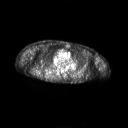
FDG PET of an extremity soft-tissue mass (from a PET/CT study), one axial slice; 3.27 mm slice thickness; 128 × 128 image matrix, field of view 700 × 700 mm. Patient: male, 61 years. From the clinical record (not read from this slice): histological type: pleiomorphic spindle cell undifferentiated; grade: high; site of the primary tumour: right parascapusular.
Outlined on this slice (expert contour drawn on MRI and transferred to this co-registered scan by the dataset authors):
- gross tumour volume including surrounding oedema: bounding box <46,73,59,78> (left, top, right, bottom; pixels)